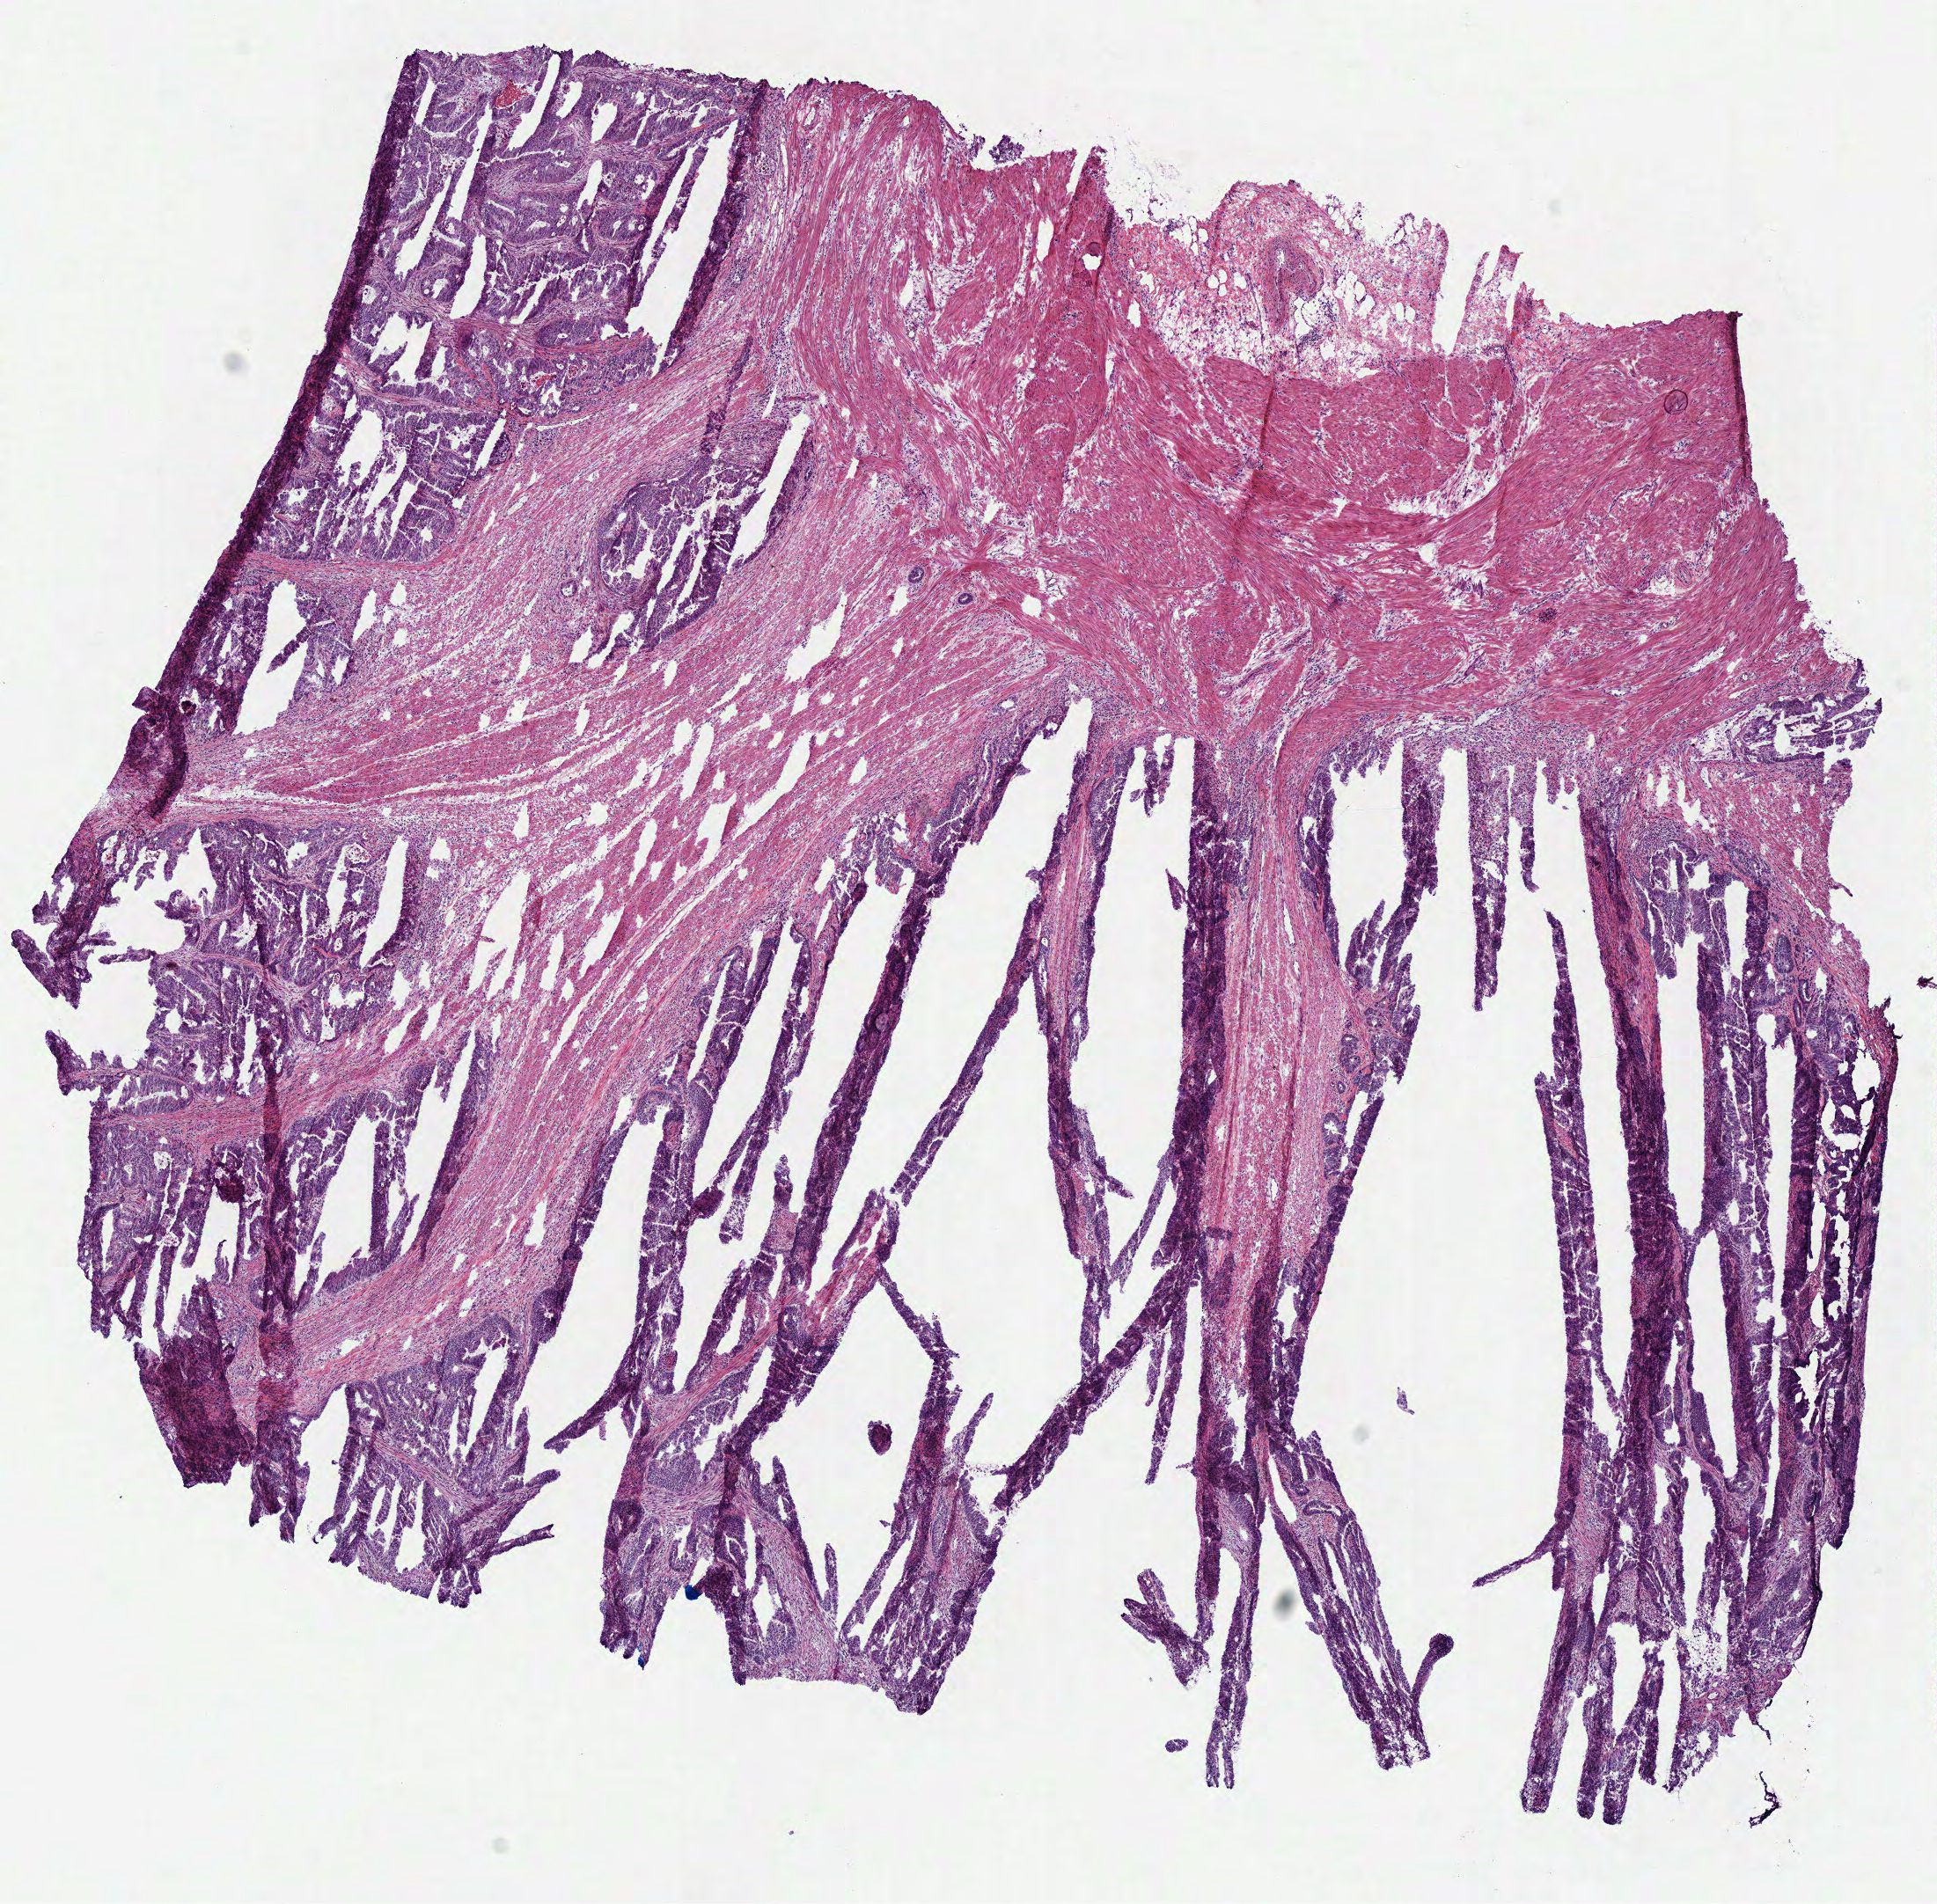
Digitized H&E-stained tissue section (whole slide), whole scanned area (about 8.7 x 8.5 mm, slide scanned at 40x) shown as a low-resolution overview; frozen section from the bottom of the tissue portion; sample: primary tumour, colon. Patient: male, age at initial diagnosis 76 years. Pathologist review of this section (percent, as recorded): tumour cells 50%, tumour nuclei 70%, normal cells 20%, stromal cells 30%, necrosis 0%. Infiltration values recorded for this section: lymphocyte infiltration 1%, monocyte infiltration 0%, neutrophil infiltration 0%.
Pathologic diagnosis: Adenocarcinoma, NOS (sigmoid colon). AJCC pathologic stage: IIIA (7th edition). Lymph nodes positive (case pathology): 1 of 8 examined.